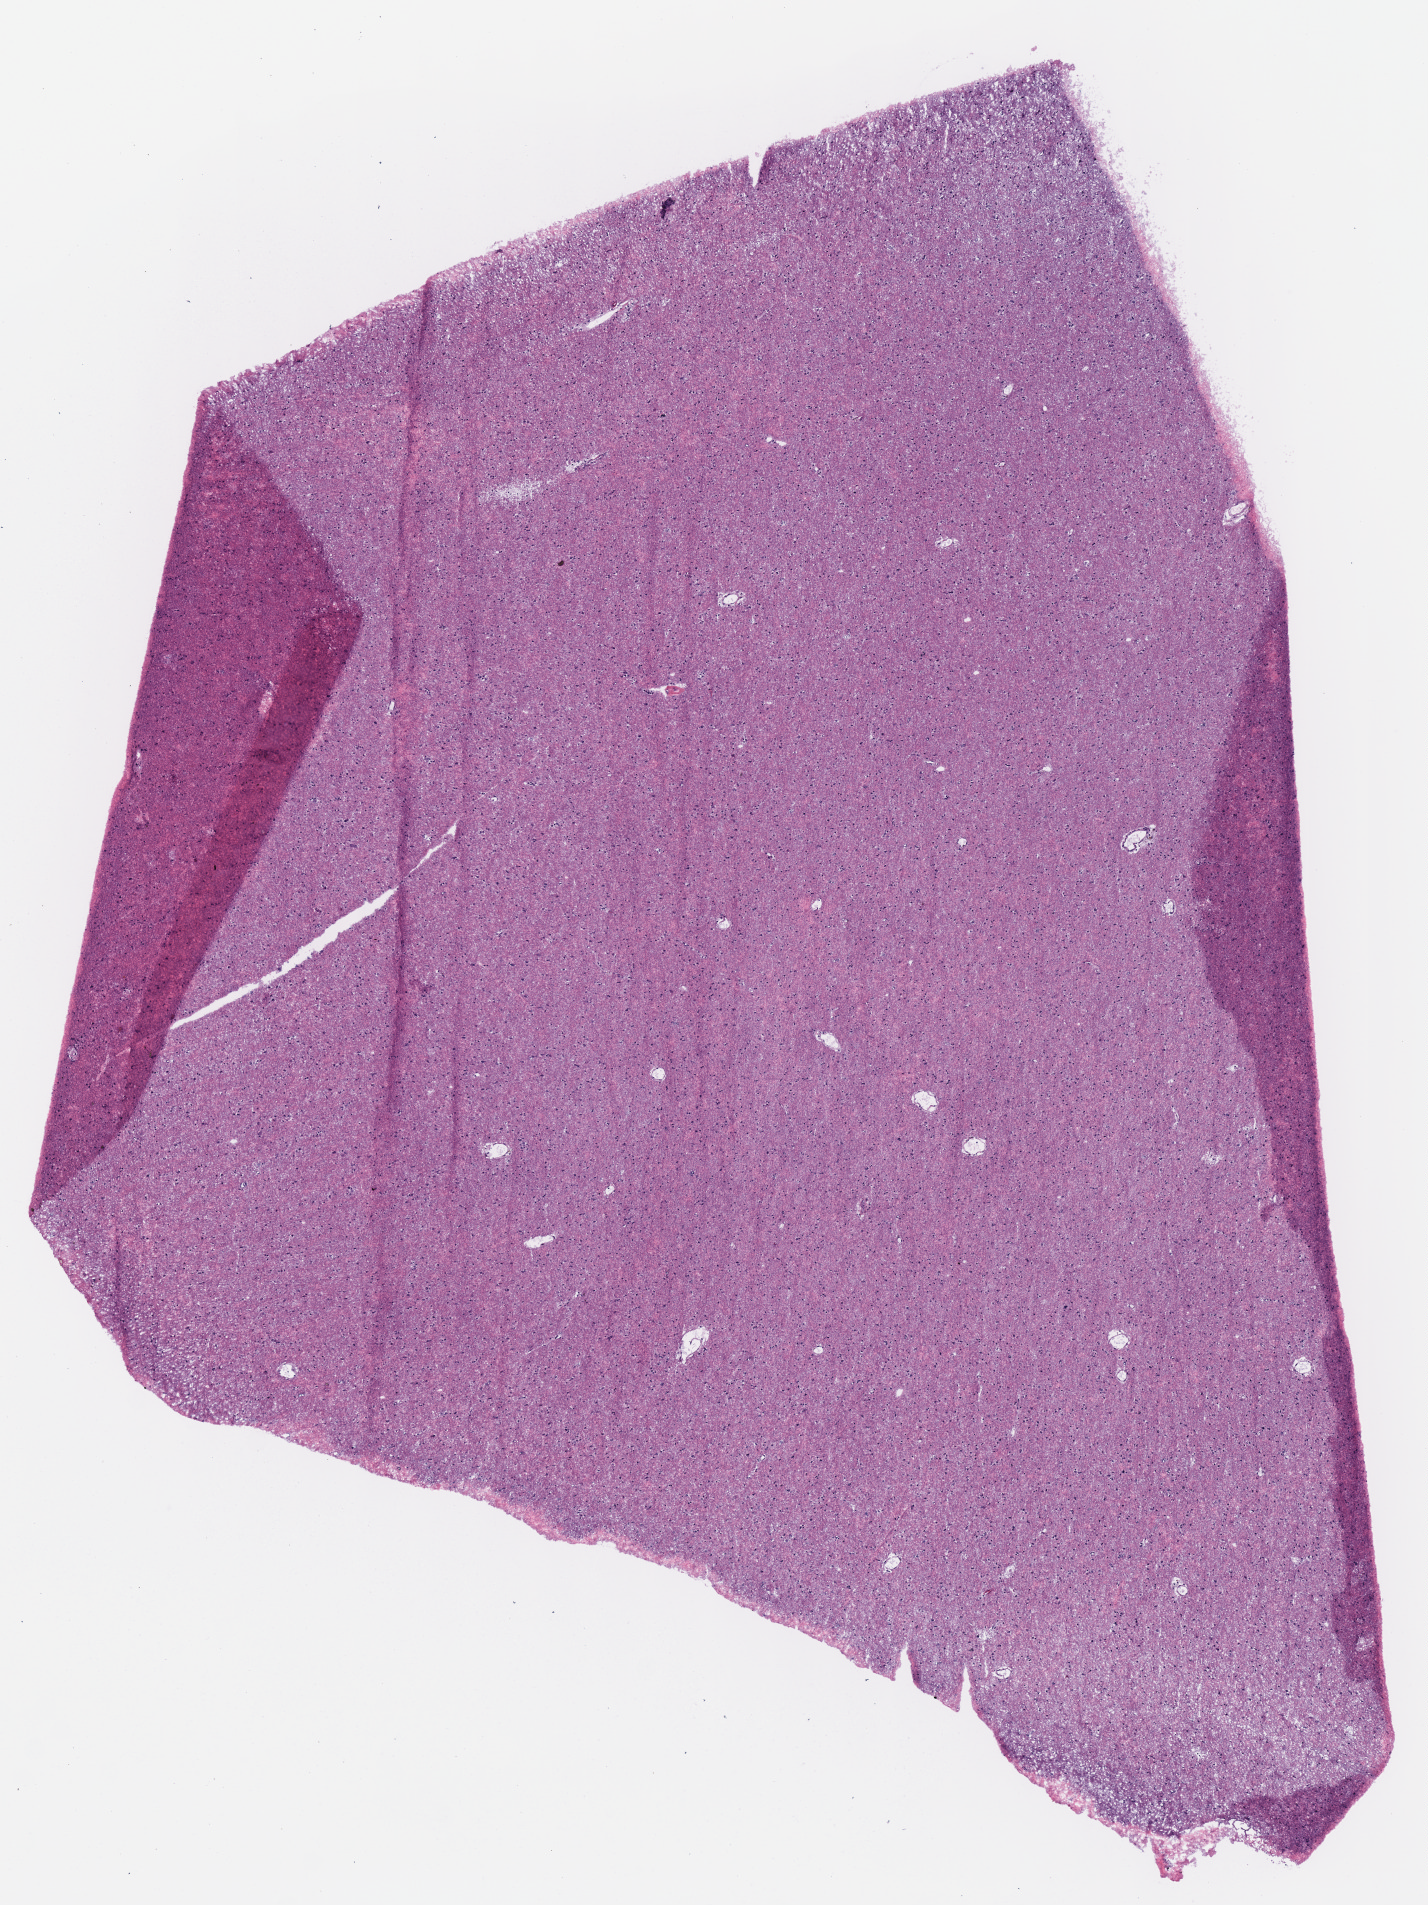
H&E-stained whole-slide image, low-resolution overview of the scanned area, about 5.6 x 7.5 mm (slide scanned at 40x), frozen section, sample: primary tumour, brain. Female, age 30 years at initial diagnosis. Histologic grade: G2 (moderately differentiated). Pathologist review of this section (percent, as recorded): tumour cells 100%, tumour nuclei 60%, normal cells 0%, stromal cells 0%, necrosis 0%.
Diagnosis: Mixed glioma (cerebrum).